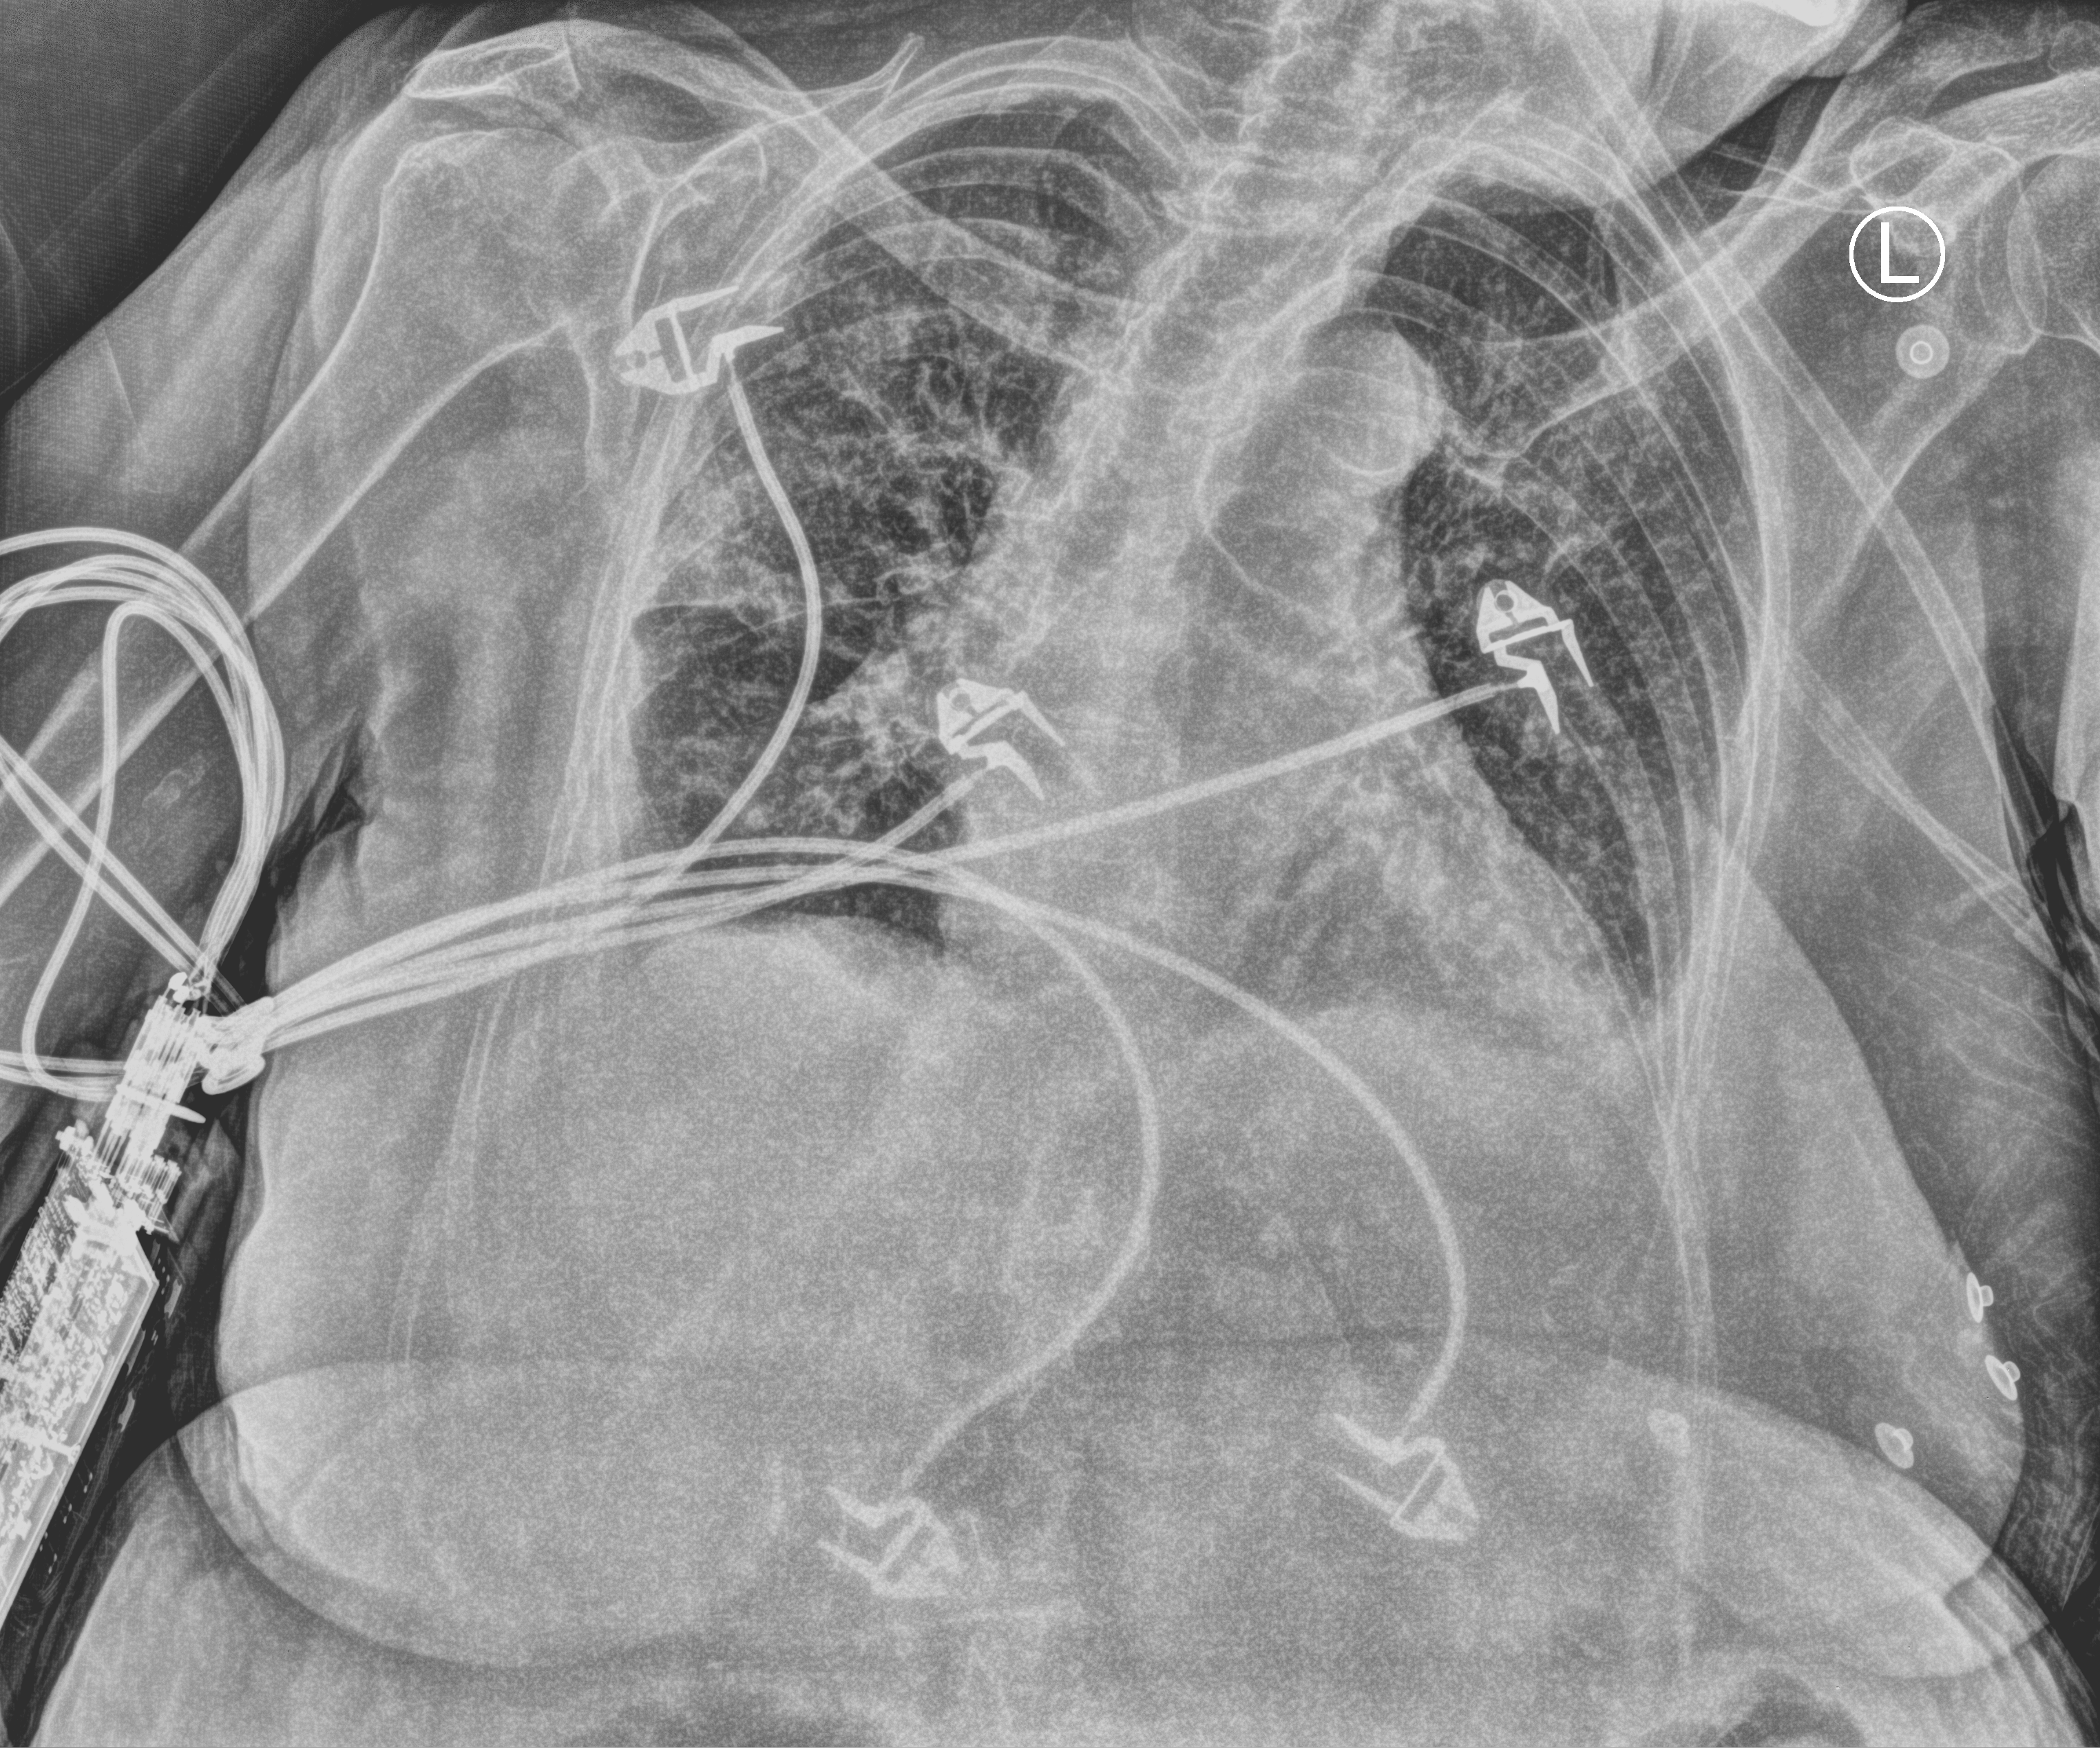
Portable chest radiograph, anteroposterior (AP) projection. Female patient hospitalised with COVID-19, age 75–90 years.
From the hospital-stay record, not from the radiograph (when in the stay this image was taken is not recorded): mechanically ventilated during this hospital stay: no.